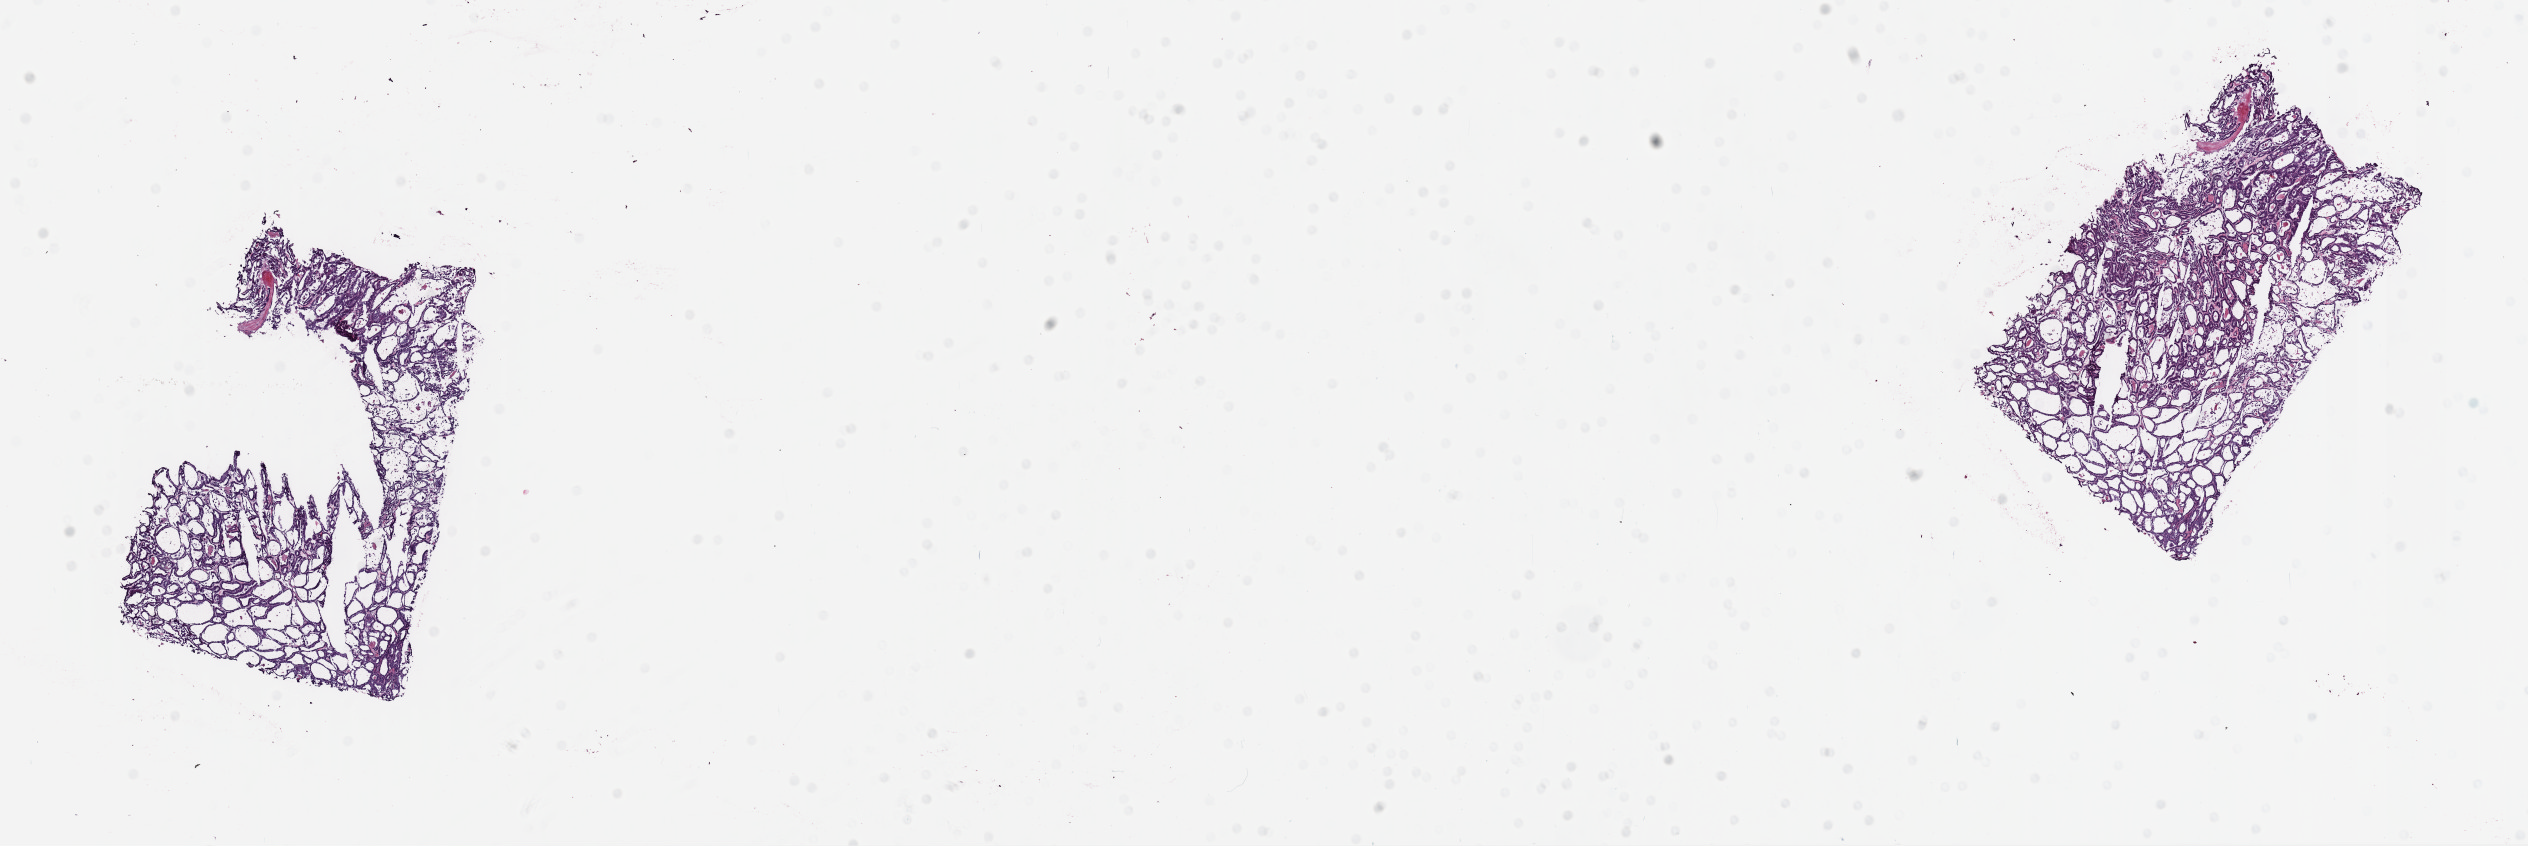
Whole-slide histology image, Hematoxylin and eosin (H&E) stained — low-resolution overview of the scanned area, about 20.0 x 6.7 mm, frozen section from the top of the tissue portion, primary tumour sample from the thyroid. Female, age 73 years at initial diagnosis. Slide review estimates, as recorded: tumour cells 95%, tumour nuclei 100%, normal cells 0%, stromal cells 5%, necrosis 0%. Inflammatory infiltration, as recorded: lymphocyte infiltration 1%, monocyte infiltration 1%, neutrophil infiltration 0%.
AJCC pathologic stage: III. TNM: T3 N0 MX. Lymph nodes positive (case pathology): 0 of 2 examined. Diagnosis: Papillary adenocarcinoma, NOS (thyroid gland).